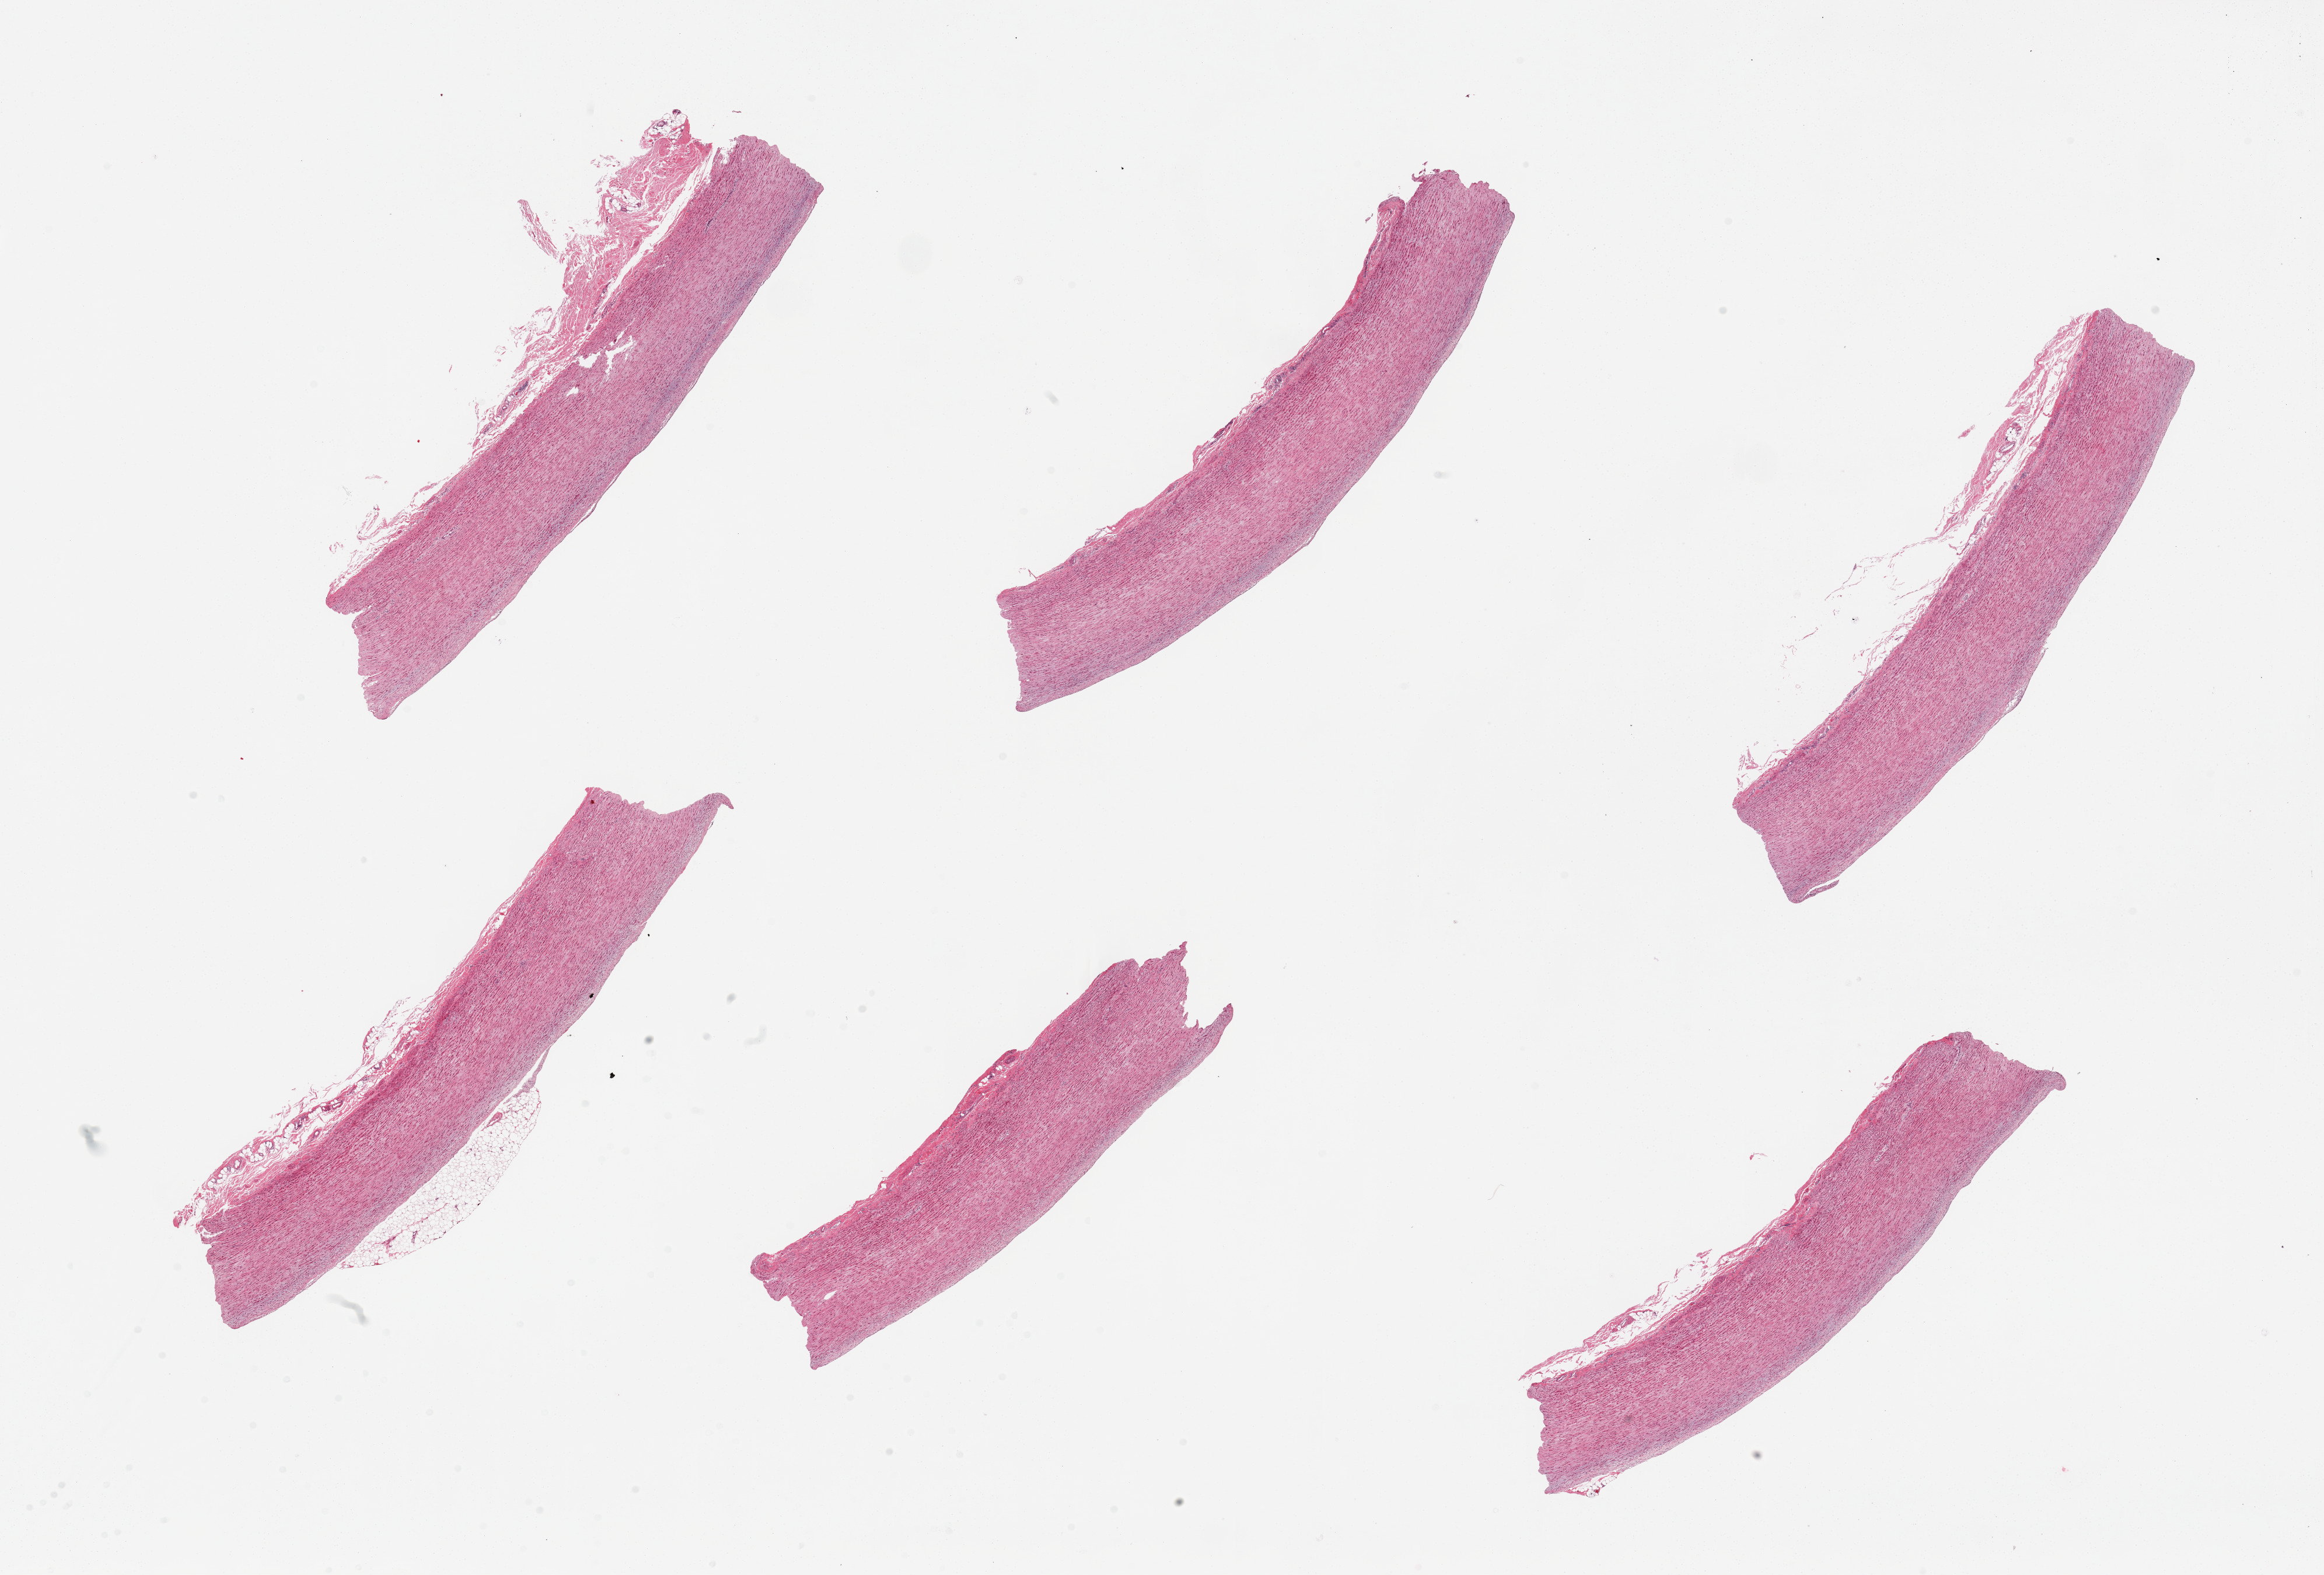
Hematoxylin and eosin (H&E) whole-slide image, low-resolution overview of the scanned area, about 31.5 x 21.3 mm (from a 20x scan), PAXgene-fixed paraffin-embedded (PFPE) section, target tissue: aorta, donor tissue sample. Donor sex: male.
Review note (as recorded): 6 pieces, from 7x2 to 9x2.5mm; well trimmed.